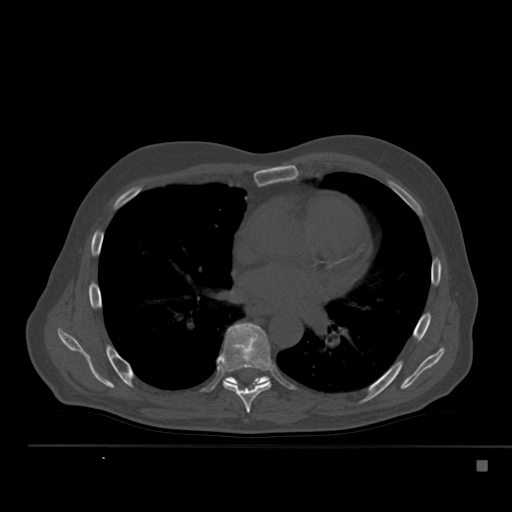
CT including the spine, one axial slice. Bone window (W 1800 / L 400 HU). 1.5 mm slice thickness. 512 × 512 image matrix. Male patient, age 70 years. From the clinical record (not read from this slice): primary cancer: renal.
Structures marked on this image (semi-automatically segmented with operator editing):
- T7 vertebra: bounding box (x1, y1, x2, y2) in pixels: (219, 323, 271, 413)
- T8 vertebra: (225, 376, 270, 388)